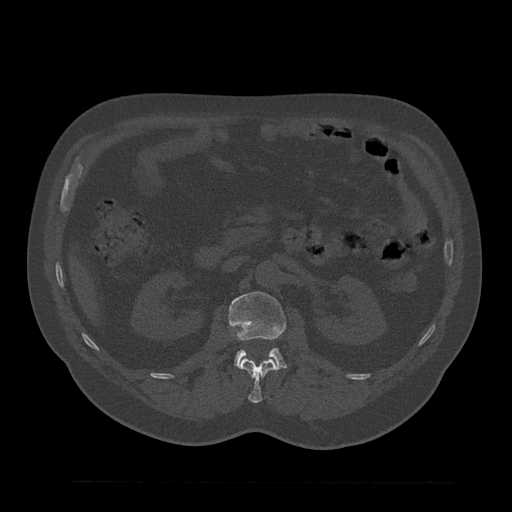
CT including the spine, one axial slice; slice 131 of 797 in the series (ordered by position); reconstruction kernel Br40s/3; bone window (W 1800 / L 400 HU); 512 × 512 image matrix, field of view 430 × 430 mm. Patient: male, 61 years. Case-level facts recorded for this patient, not image findings: primary cancer: prostate.
Structures marked on this image (semi-automatically segmented with operator editing):
- L1 vertebra: bounding box (x1, y1, x2, y2) in pixels: (240, 358, 278, 403)
- L2 vertebra: (229, 291, 286, 369)